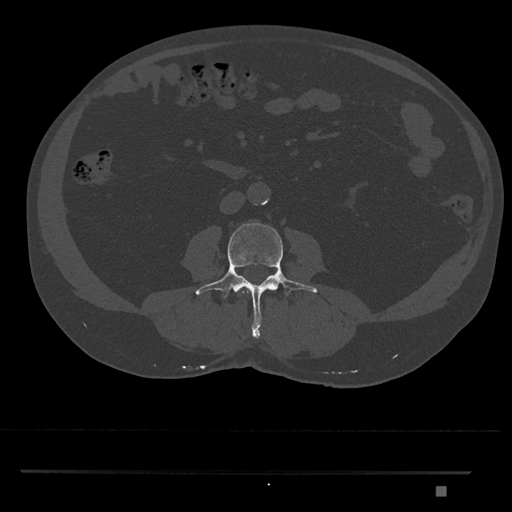
CT including the spine, one axial slice. Slice 682 of 1134 in the series (ordered by position). Bone window (W 1800 / L 400 HU). 512 × 512 image matrix, field of view 429 × 429 mm. Patient: male, 65 years. Case-level facts recorded for this patient, not image findings: primary cancer: prostate.
Structures marked on this image (semi-automatically segmented with operator editing):
- L2 vertebra: box from (x=242, y=291) to (x=245, y=294) px
- L3 vertebra: (x=195, y=222)–(x=318, y=338)